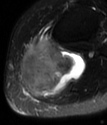
MRI of an extremity soft-tissue mass, one axial slice; slice 42 of 78 in the series (ordered by position); T2-weighted fat-saturated; MR volume resampled by the dataset authors to the PET/CT grid (not the native acquisition matrix); 3.27 mm slice thickness; 107 × 125 image matrix, field of view 104 × 122 mm. Female patient. From the clinical record (not read from this slice): histological type: extraskeletal high grade osteogenic sarcoma; grade: high; site of the primary tumour: left calf.
Annotated regions visible in this slice (expert contour drawn on MRI and transferred to this co-registered scan by the dataset authors):
- gross tumour volume (mass): bounding box <21,36,86,96> (left, top, right, bottom; pixels)